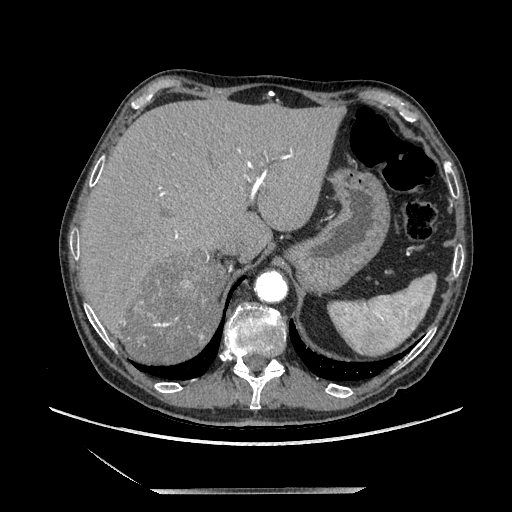
Contrast-enhanced abdominal CT, one axial slice. Slice 165 of 243 in the series (ordered by position). Soft-tissue window (W 400 / L 40 HU). 1.25 mm slice thickness. 512 × 512 image matrix, field of view 420 × 420 mm. Male patient. Case-level facts recorded for this patient, not image findings: diagnosis: adrenocortical carcinoma; tumour side: right adrenal; tumour size at pathology: 16 cm; Ki-67 index: 17 %; stage (as recorded): 3.
Annotated regions visible in this slice (semi-automatic segmentation, software-assisted and operator-edited):
- mass: bounding box <122,254,224,363> (left, top, right, bottom; pixels)